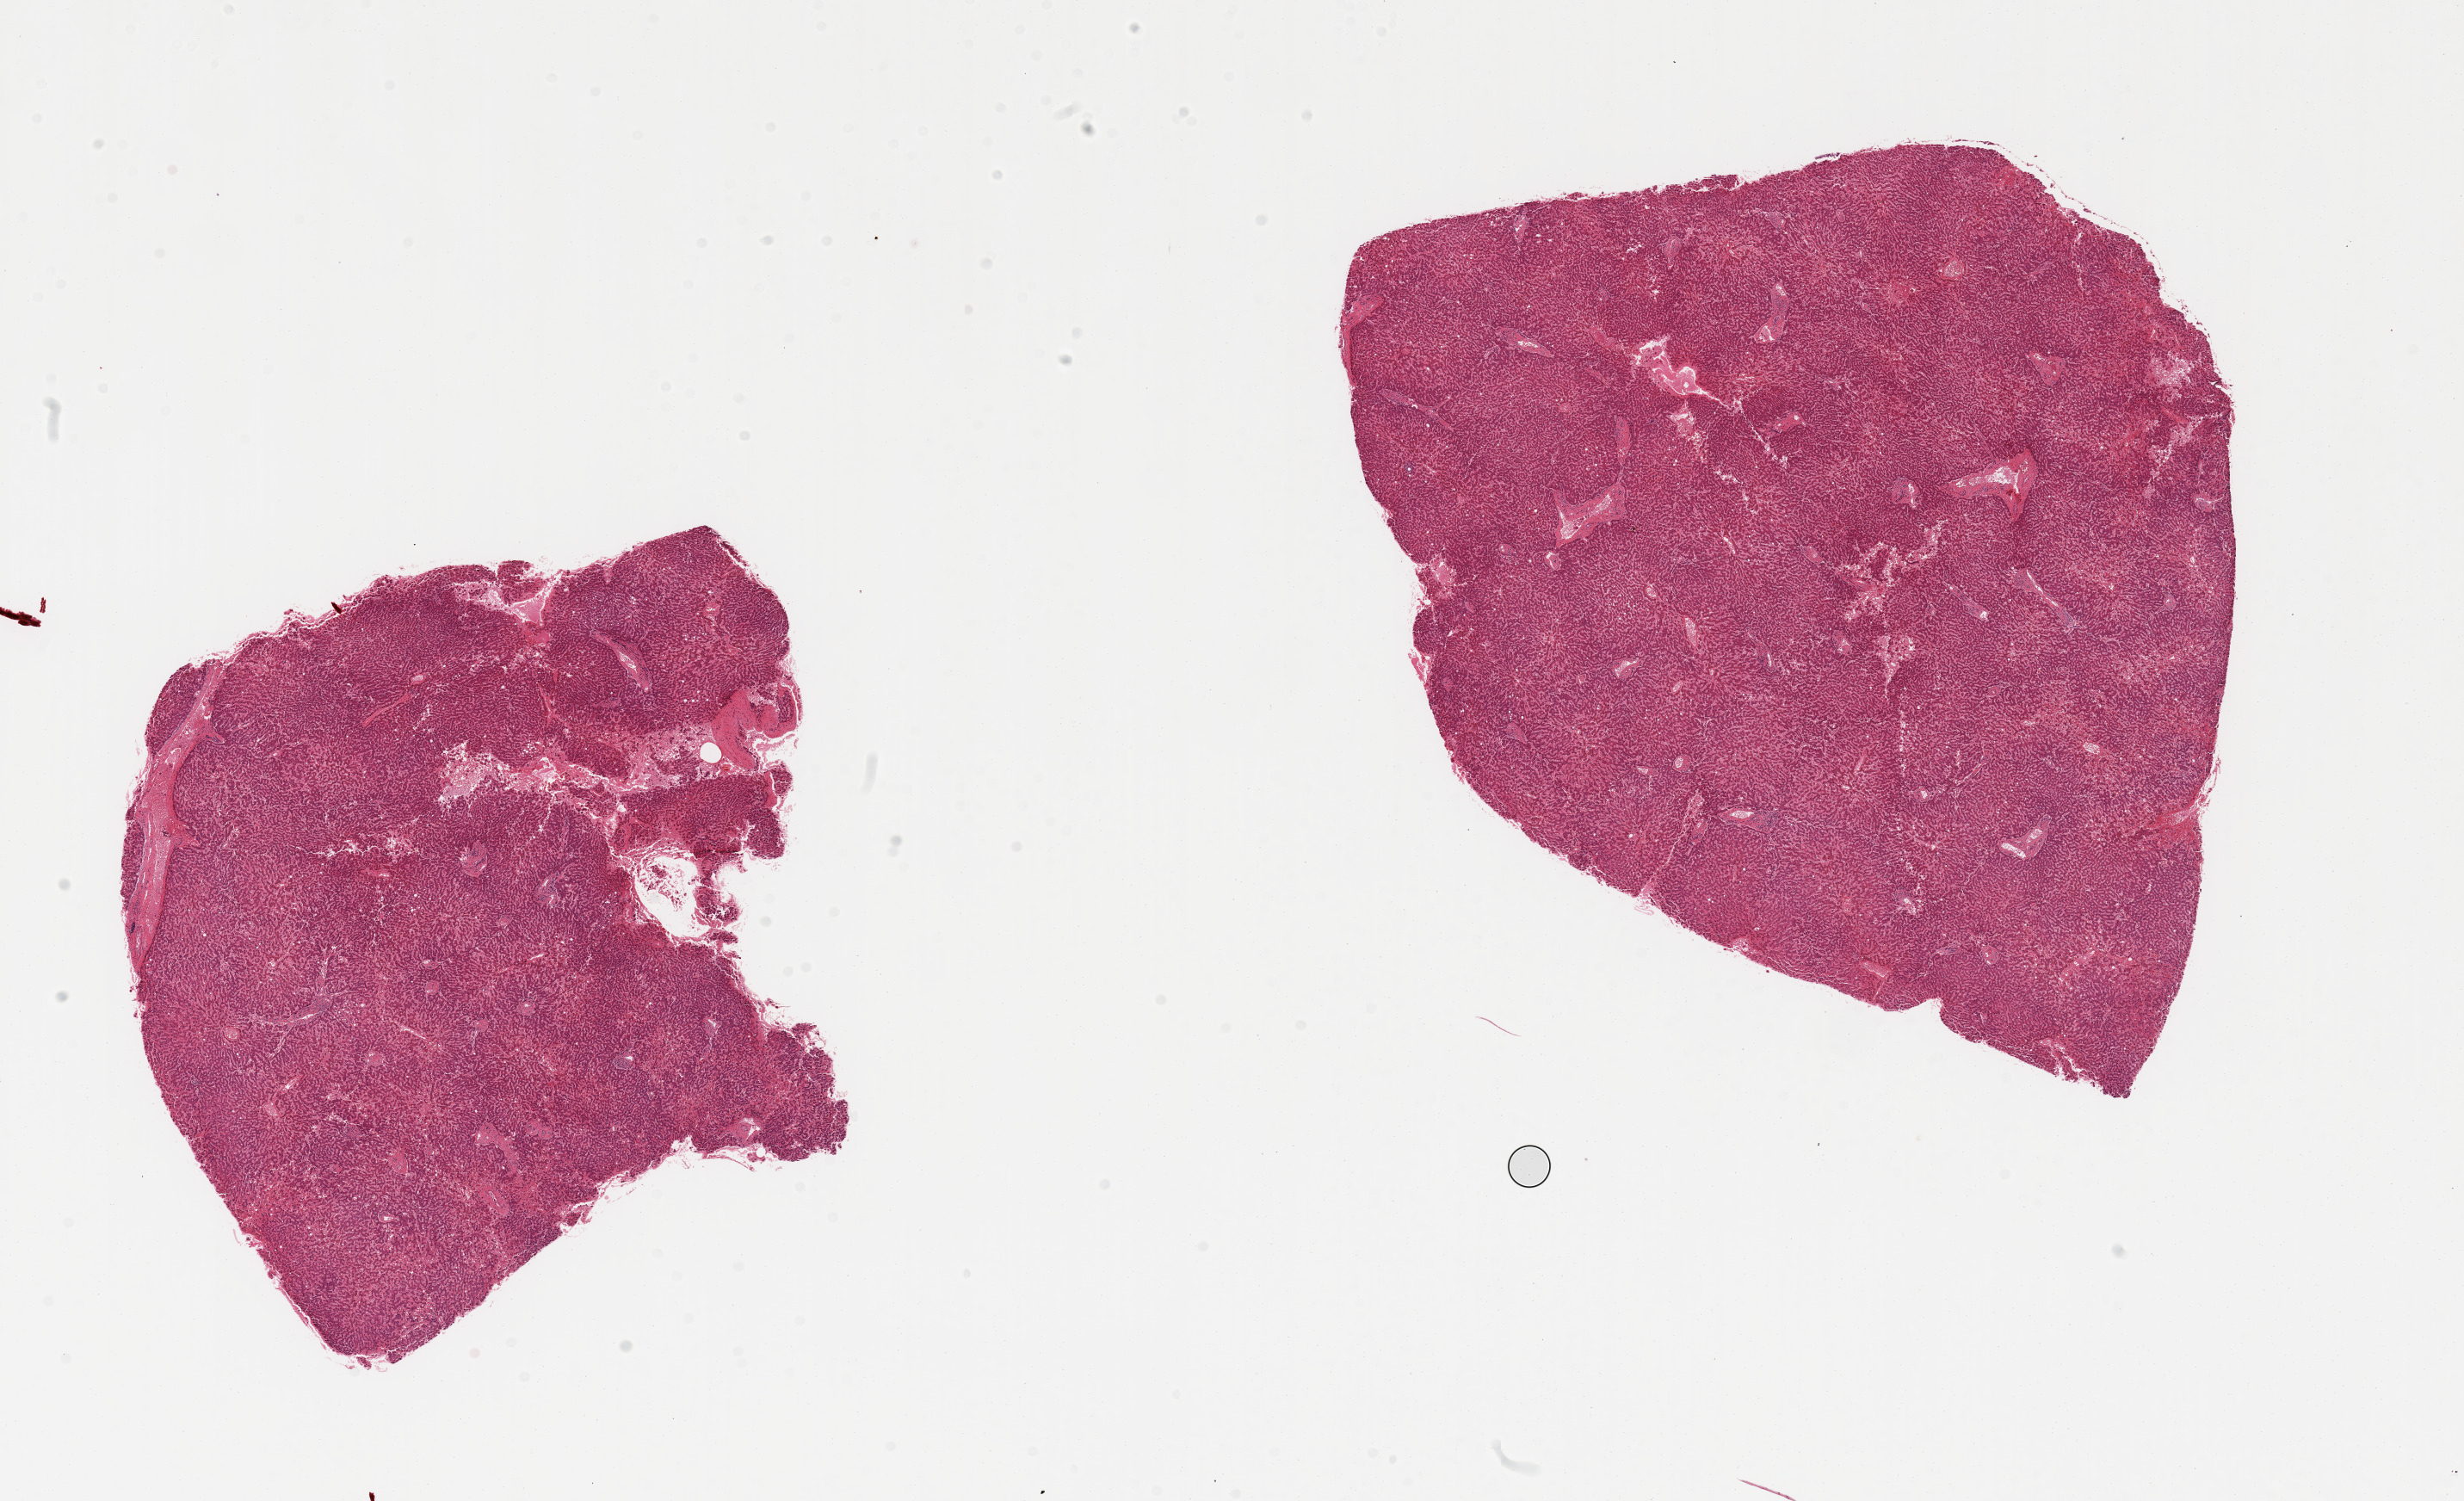
Hematoxylin and eosin (H&E) whole-slide image, low-resolution overview of the scanned area, about 22.6 x 13.8 mm, PAXgene-fixed paraffin-embedded (PFPE) section, target tissue: liver, donor tissue sample. Male donor.
Reviewer comment on this tissue sample: 2 pieces, minimal congestion/steatosis.